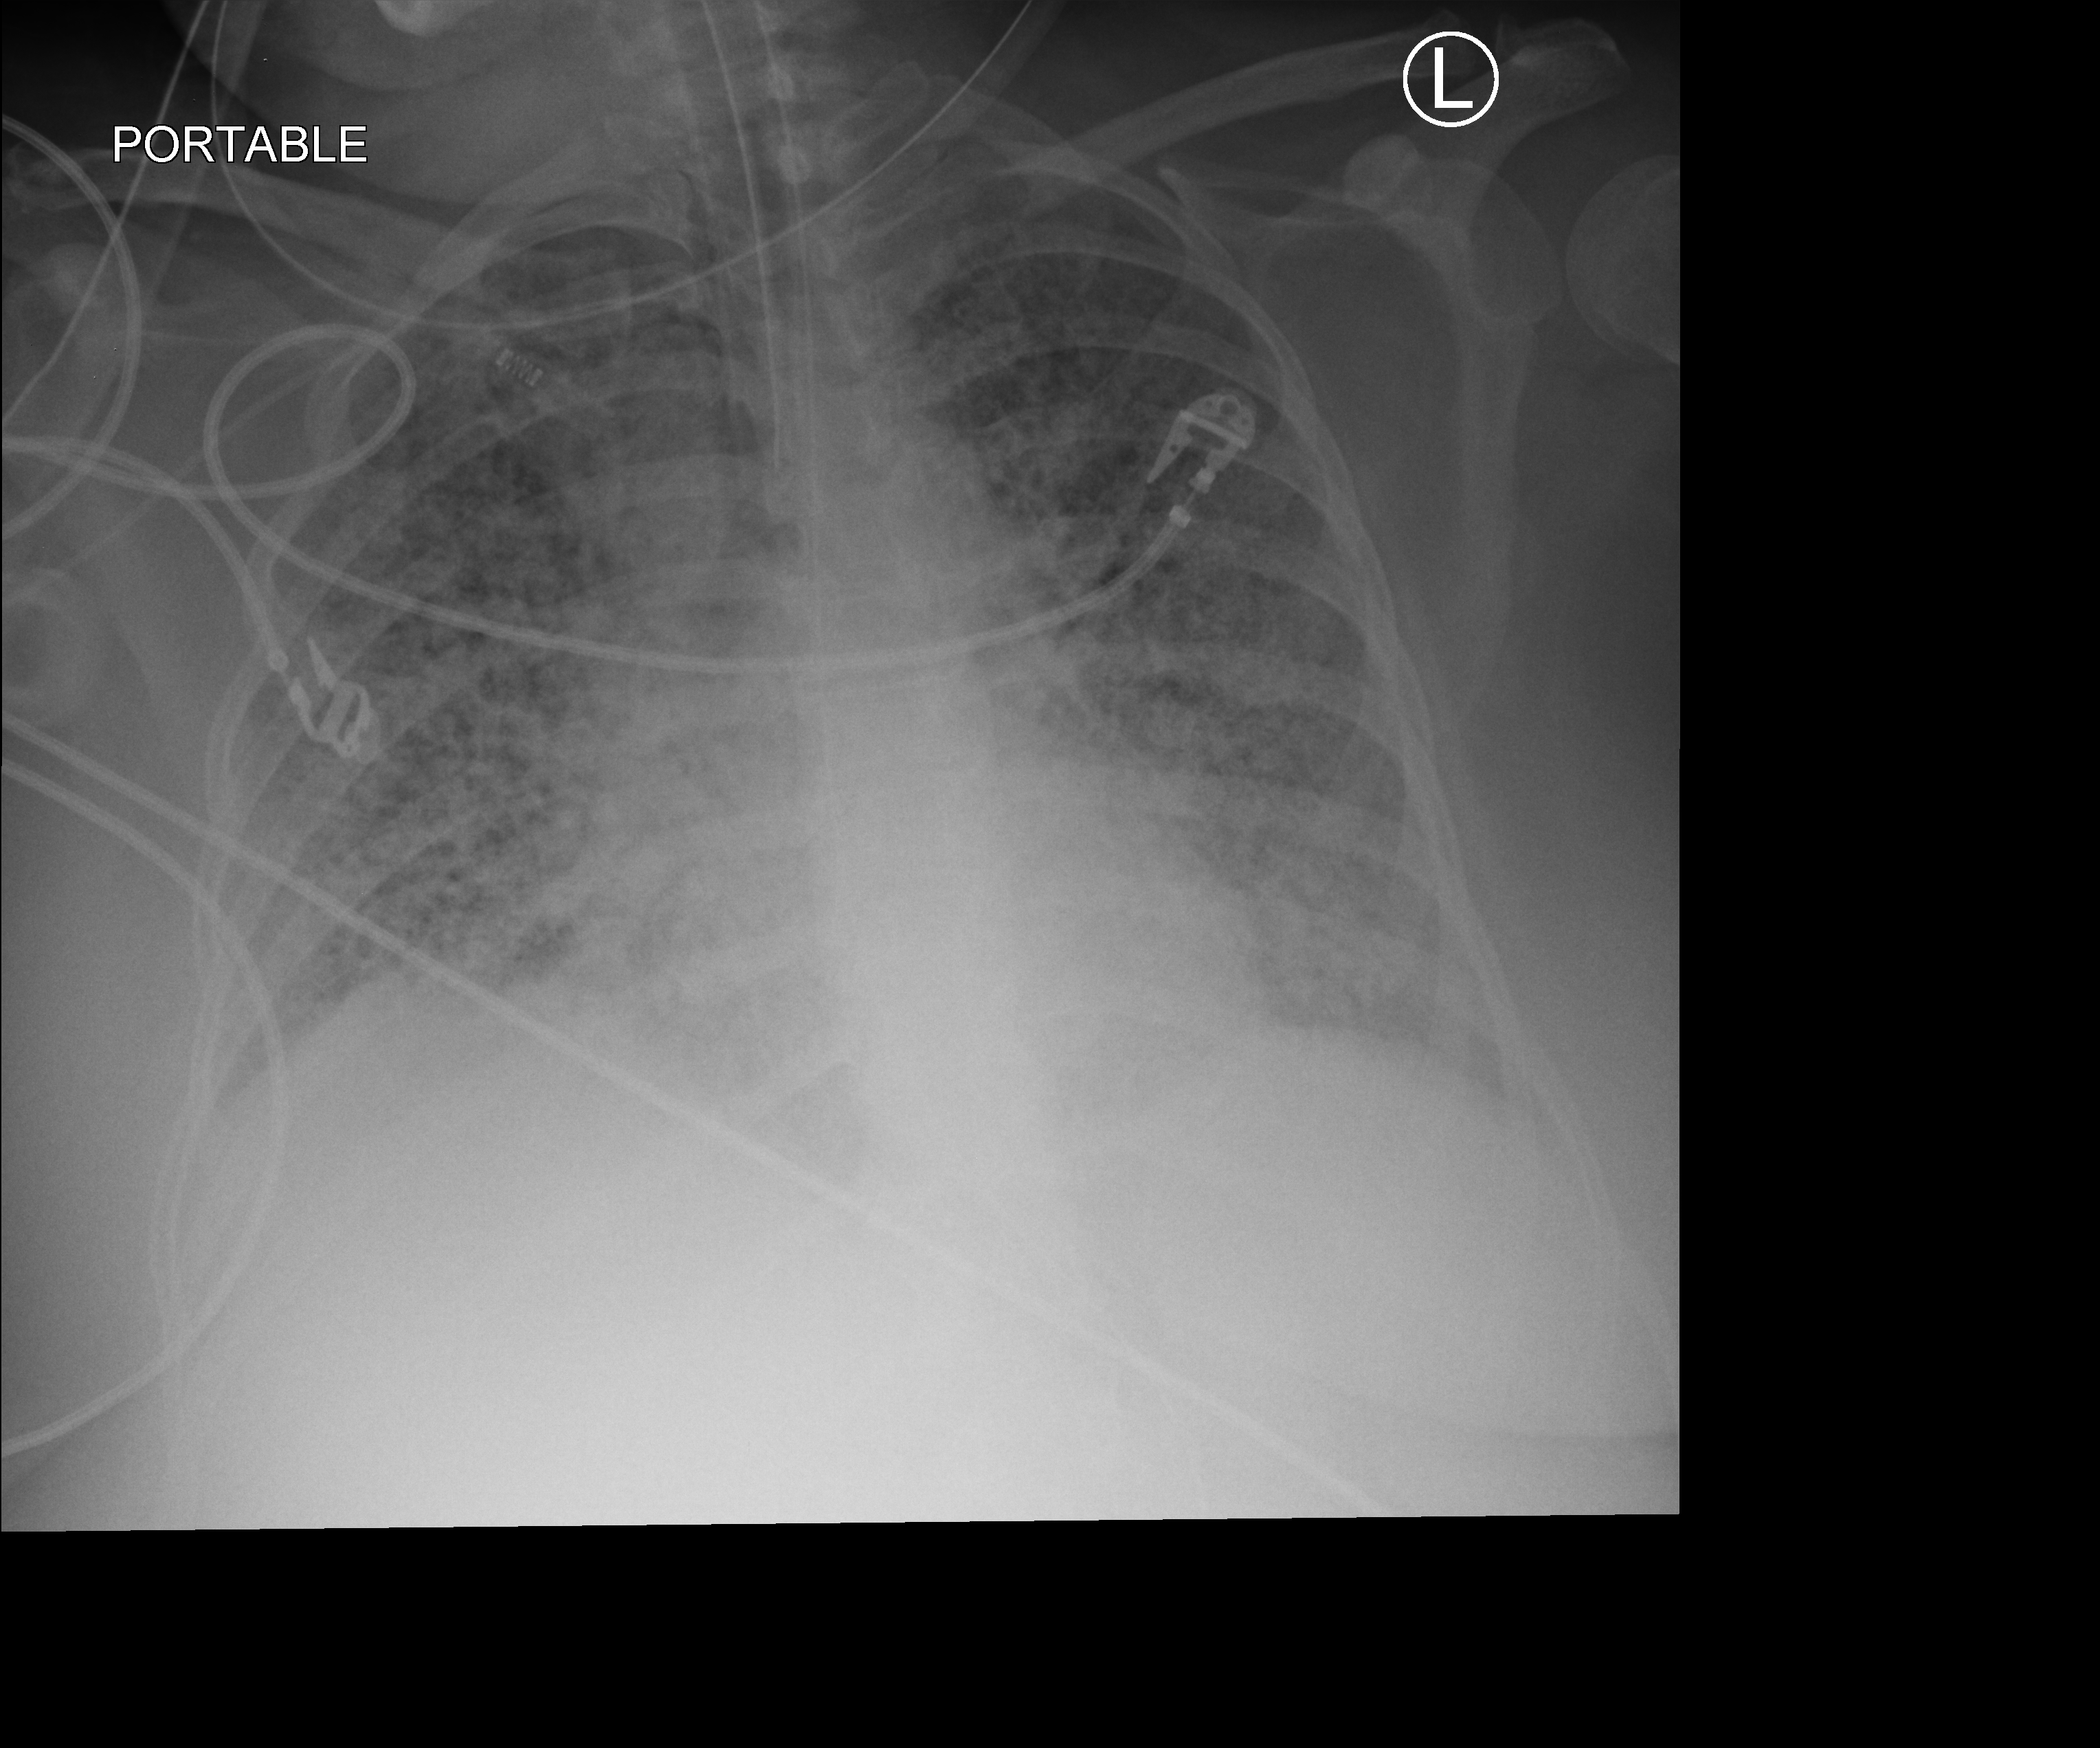
Portable chest radiograph; anteroposterior (AP) projection. Patient hospitalised with COVID-19; female, aged 18–59 years.
Admission-level facts for this patient (not findings on this image; timing relative to this image not recorded): hypertension (admission record): yes.